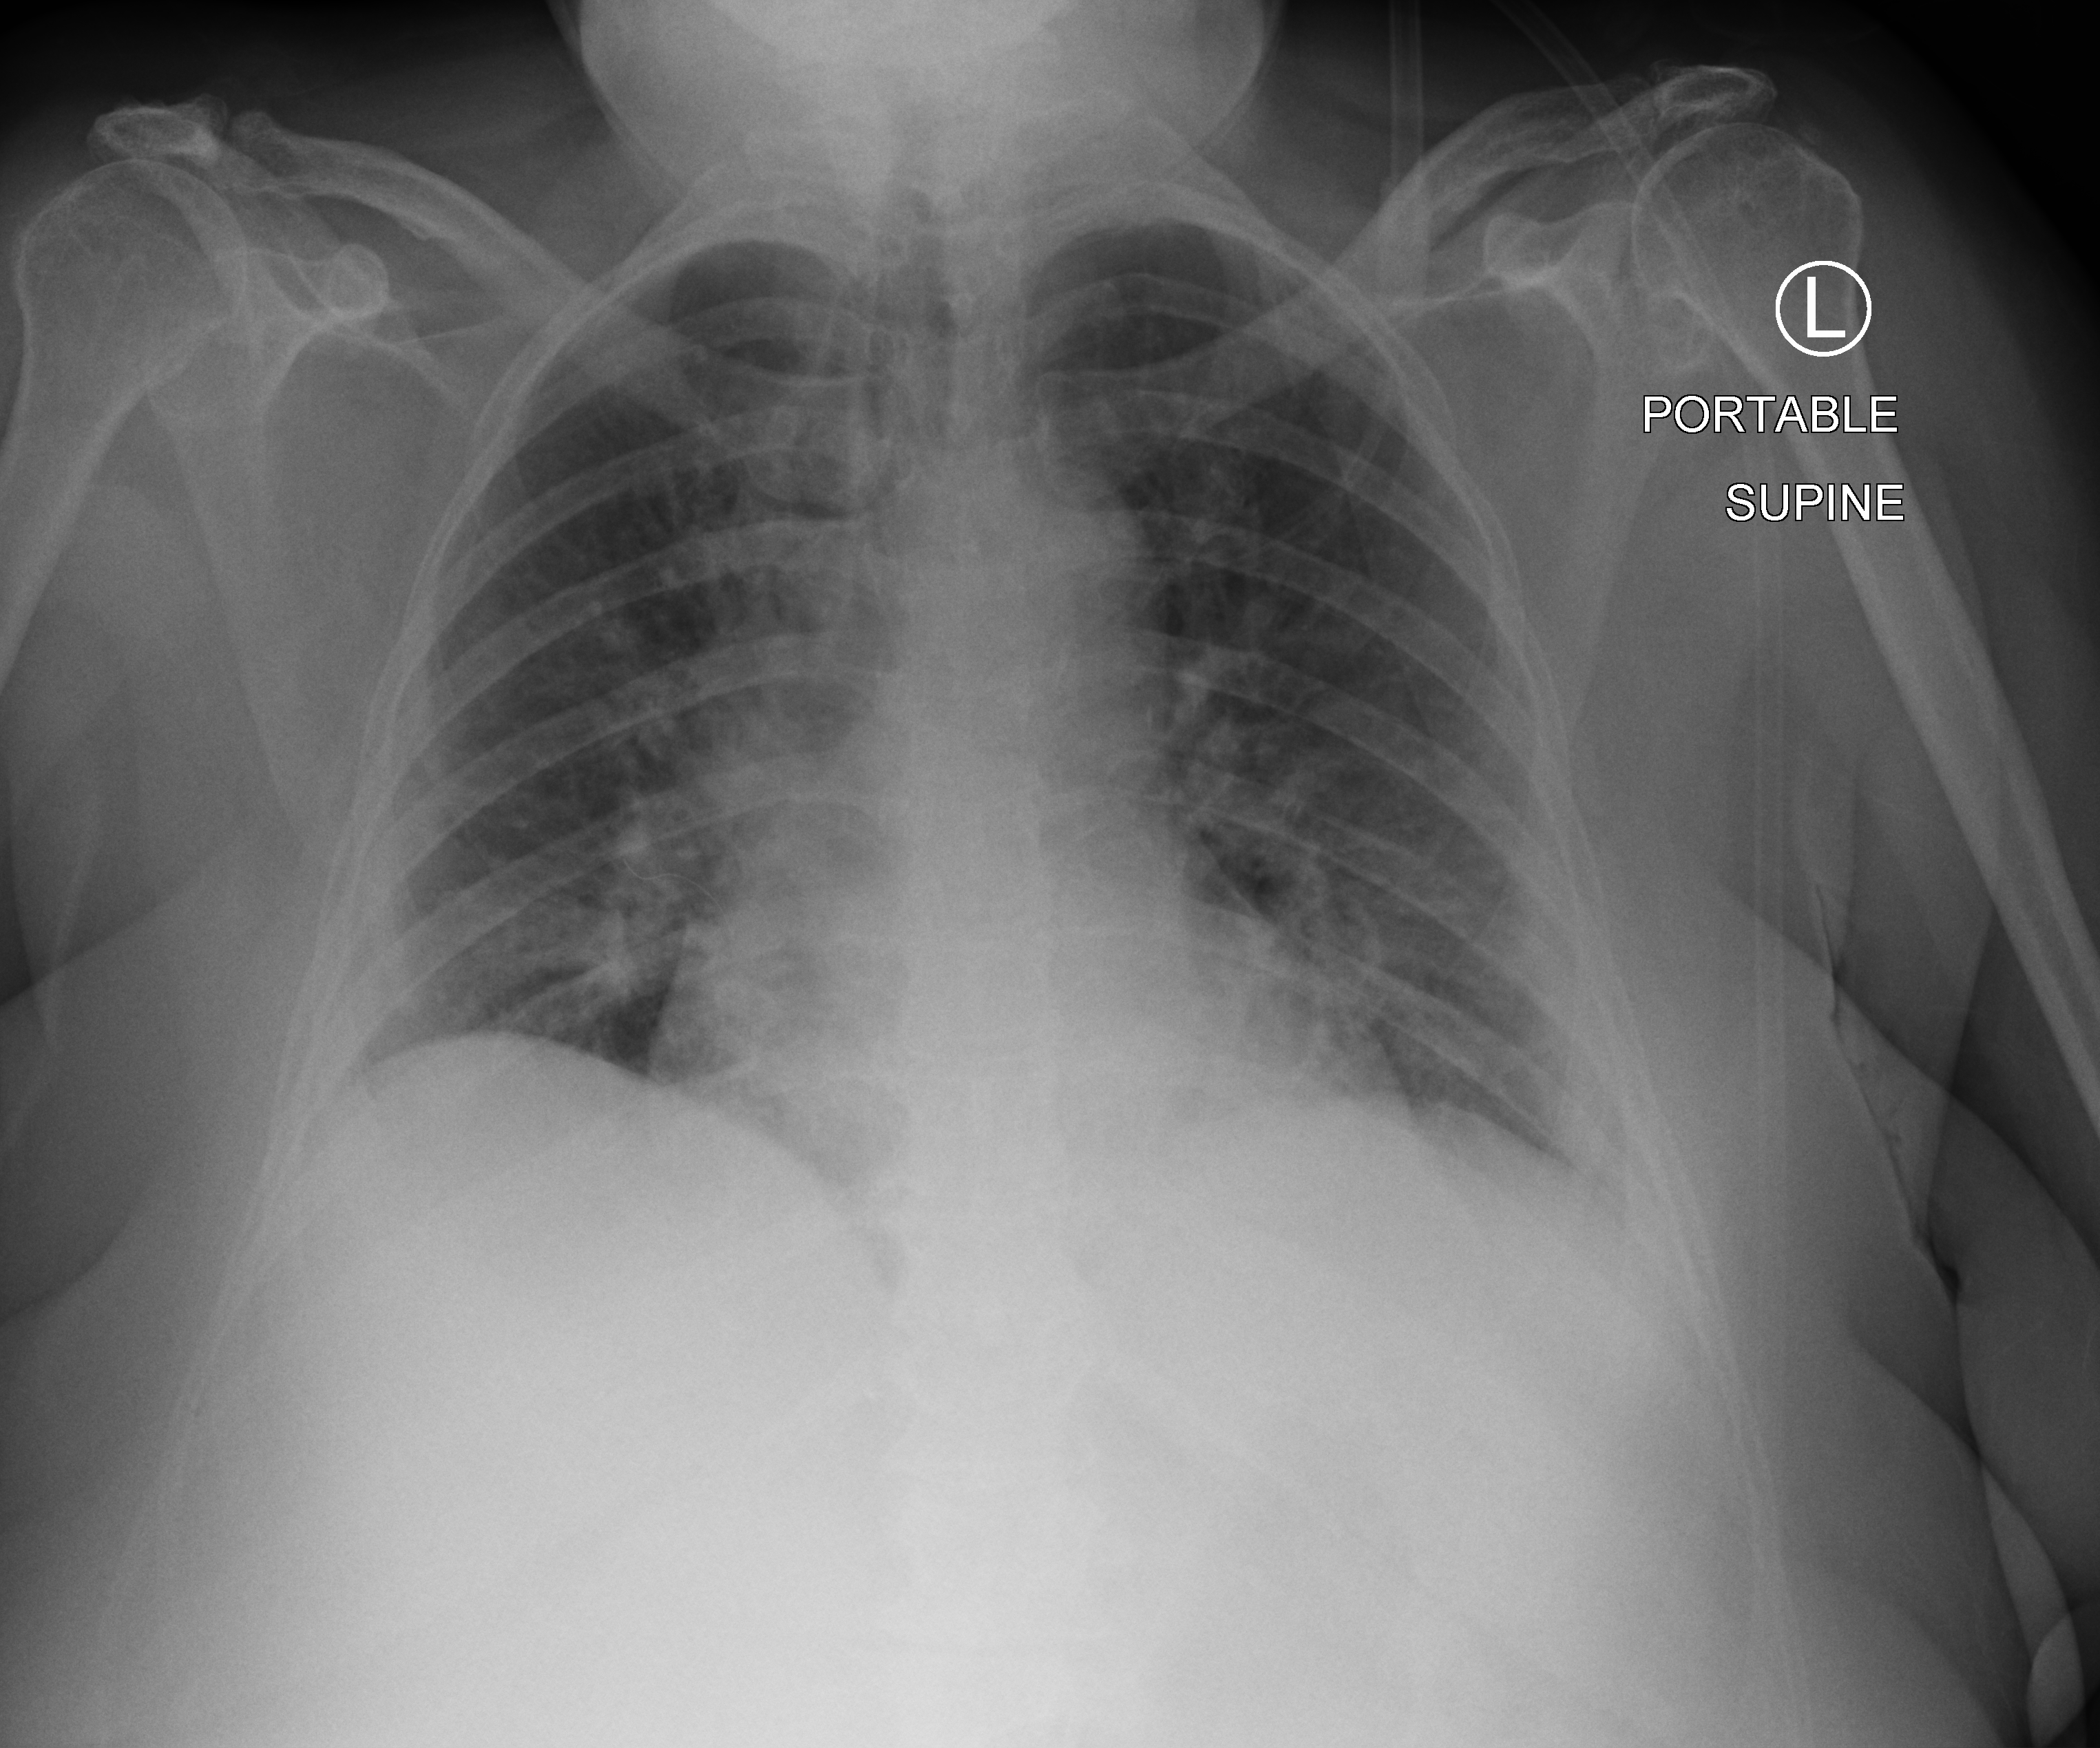
Chest X-ray (portable), anteroposterior (AP) projection. Female patient hospitalised with COVID-19, age 60–74 years.
Hospital-stay facts (about this admission, not read from this image; timing relative to this image not recorded): mechanically ventilated during this hospital stay: no.